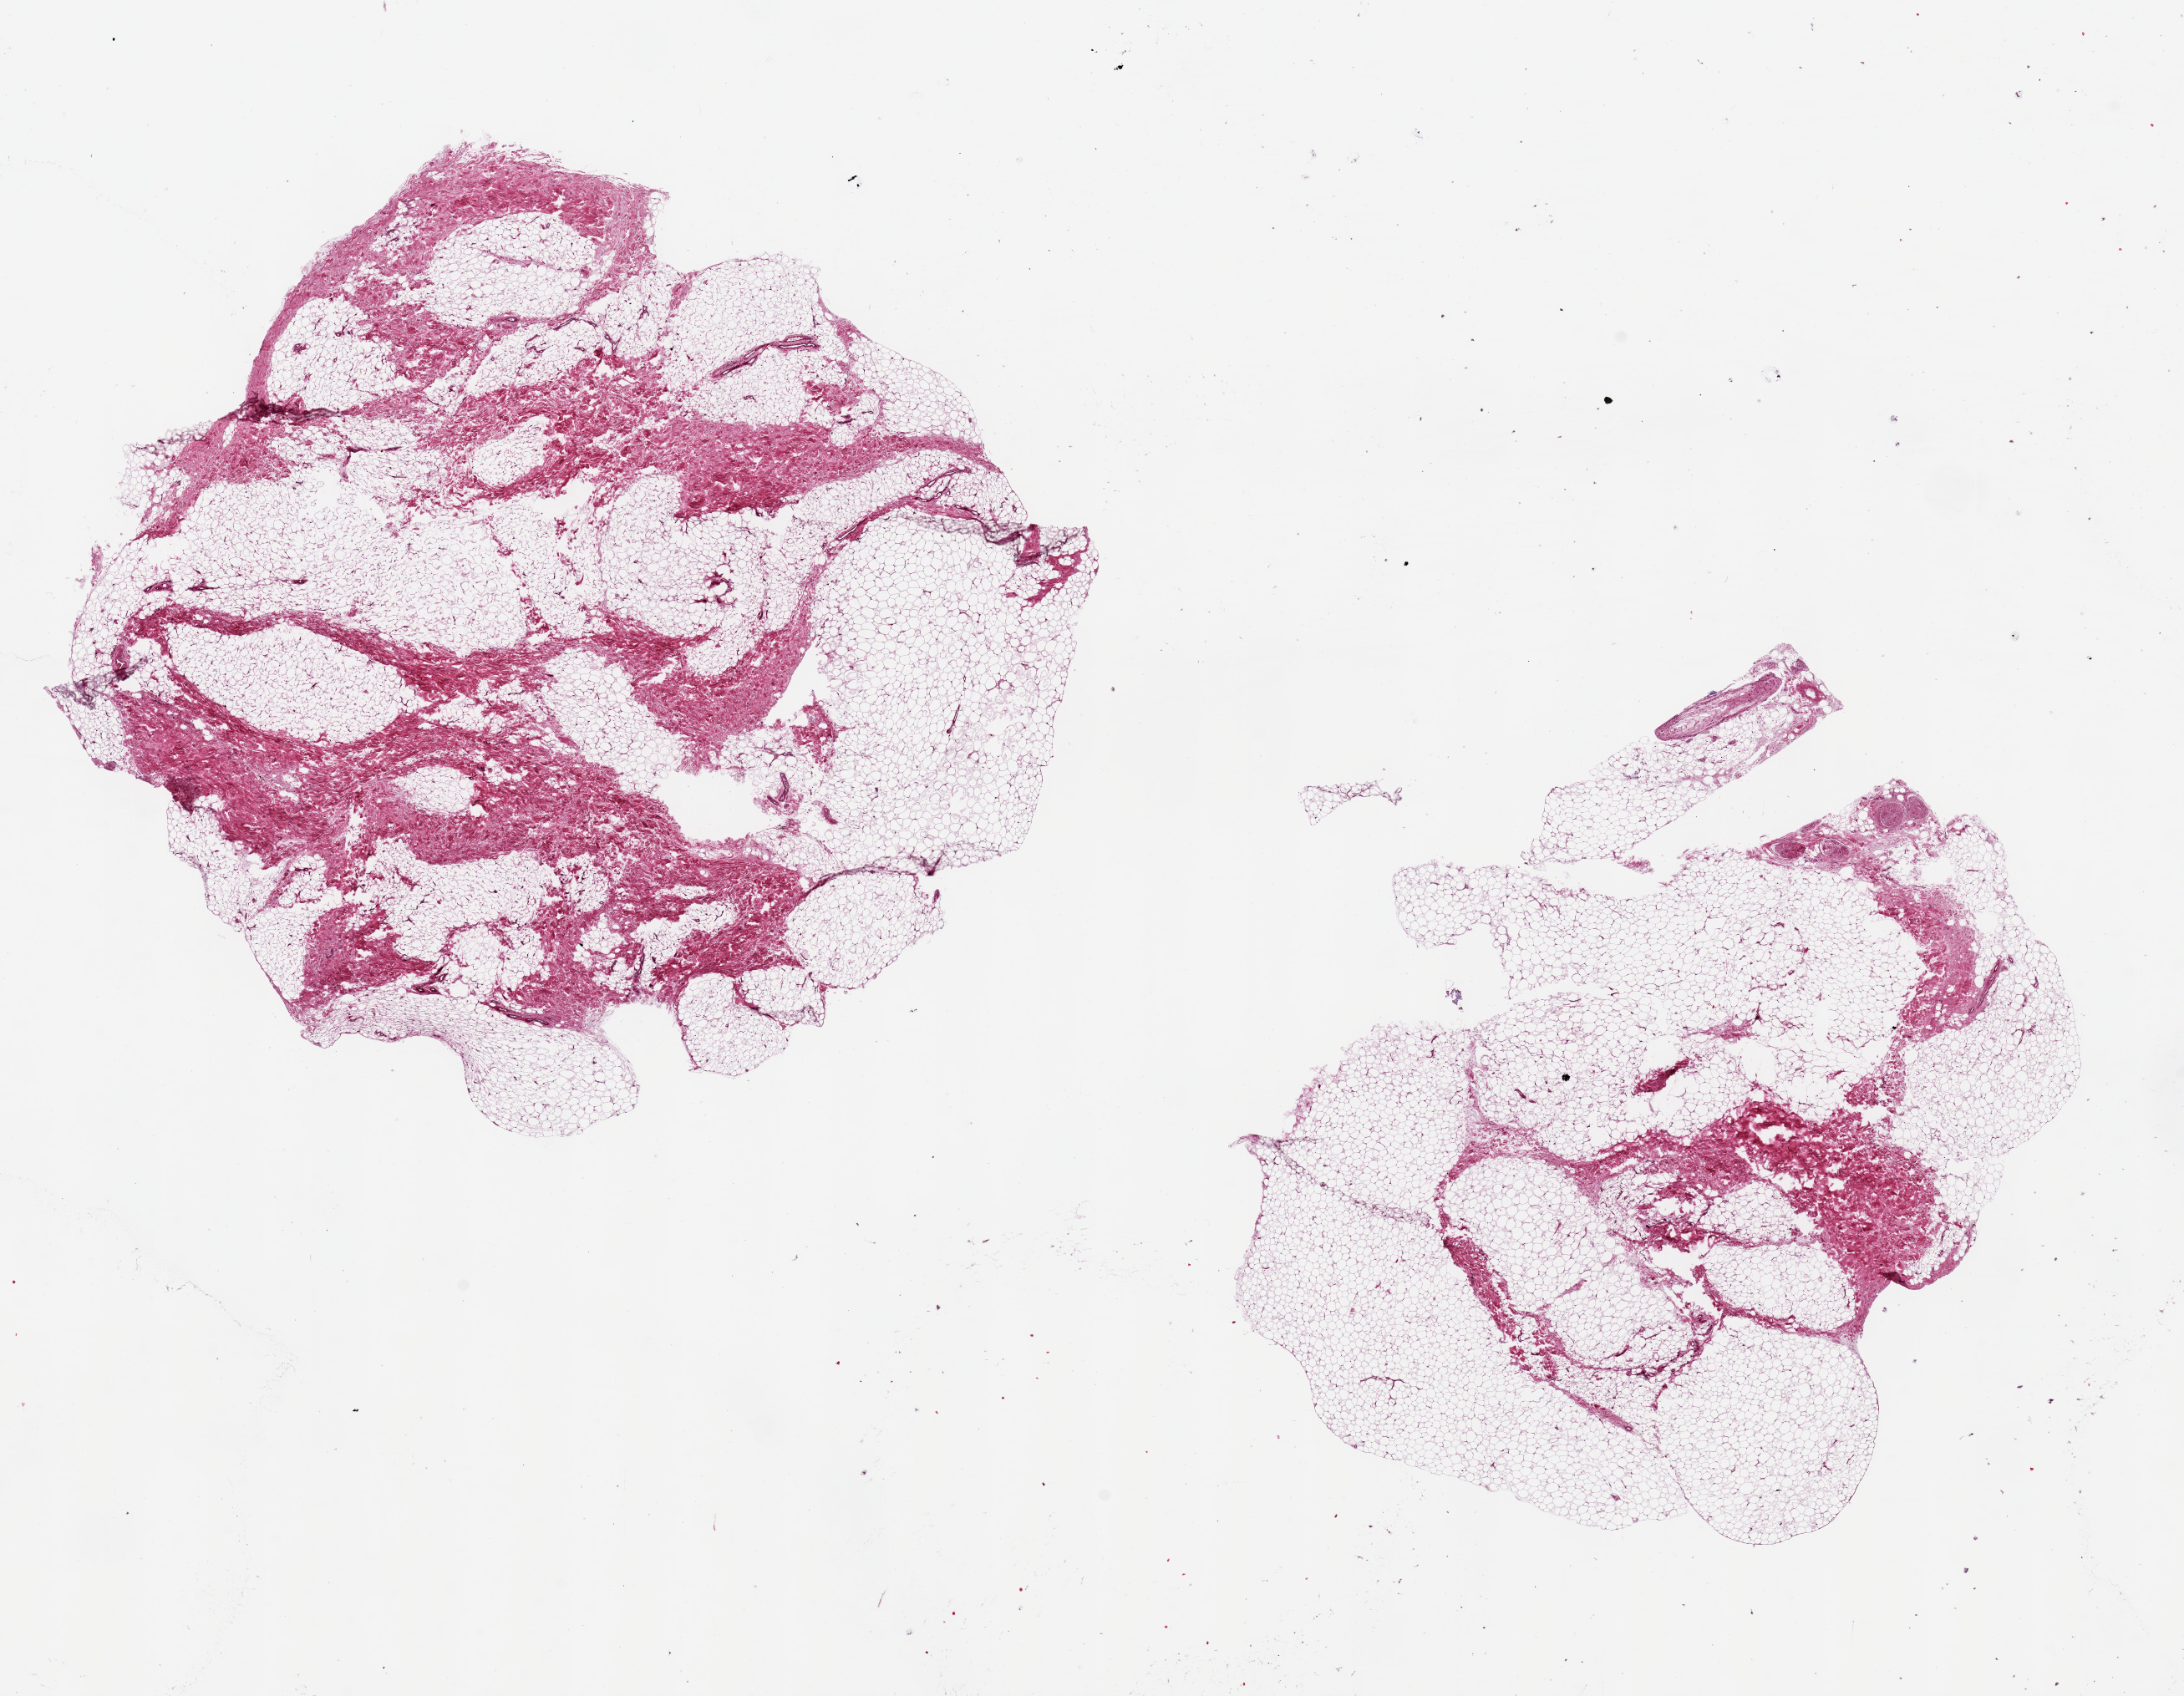
Haematoxylin and eosin whole-slide image, brightfield — low-resolution overview of the scanned area, about 20.7 x 16.1 mm (from a 20x scan), PAXgene-fixed, paraffin-embedded tissue, section of breast (target tissue), tissue donor sample.
- review note (as recorded): 2 pieces ~9x9mm, fibroadipose tissue, no ductal elements noted